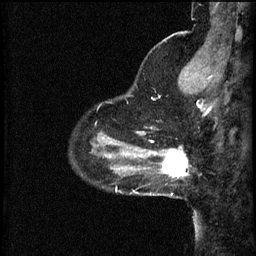
Breast MRI (dynamic contrast-enhanced), one sagittal slice. Position 12 of 60 along the scan axis. 3 images stored at this slice position (order not interpretable as contrast timing). 1.5 T. TE 4.2 ms, TR 8.2 ms. 2 mm slice thickness. 256 × 256 image matrix, field of view 200 × 200 mm. Female patient, age 37 years.
Outlined on this slice (semi-automatically segmented with operator editing):
- analysis volume of interest (the breast-tissue region the enhancement analysis was run in; not a lesion): bounding box <148,140,189,195> (left, top, right, bottom; pixels)
- tumour enhancement mask (voxels above the 70 % enhancement threshold inside the analysis volume of interest): <156,150,189,177>